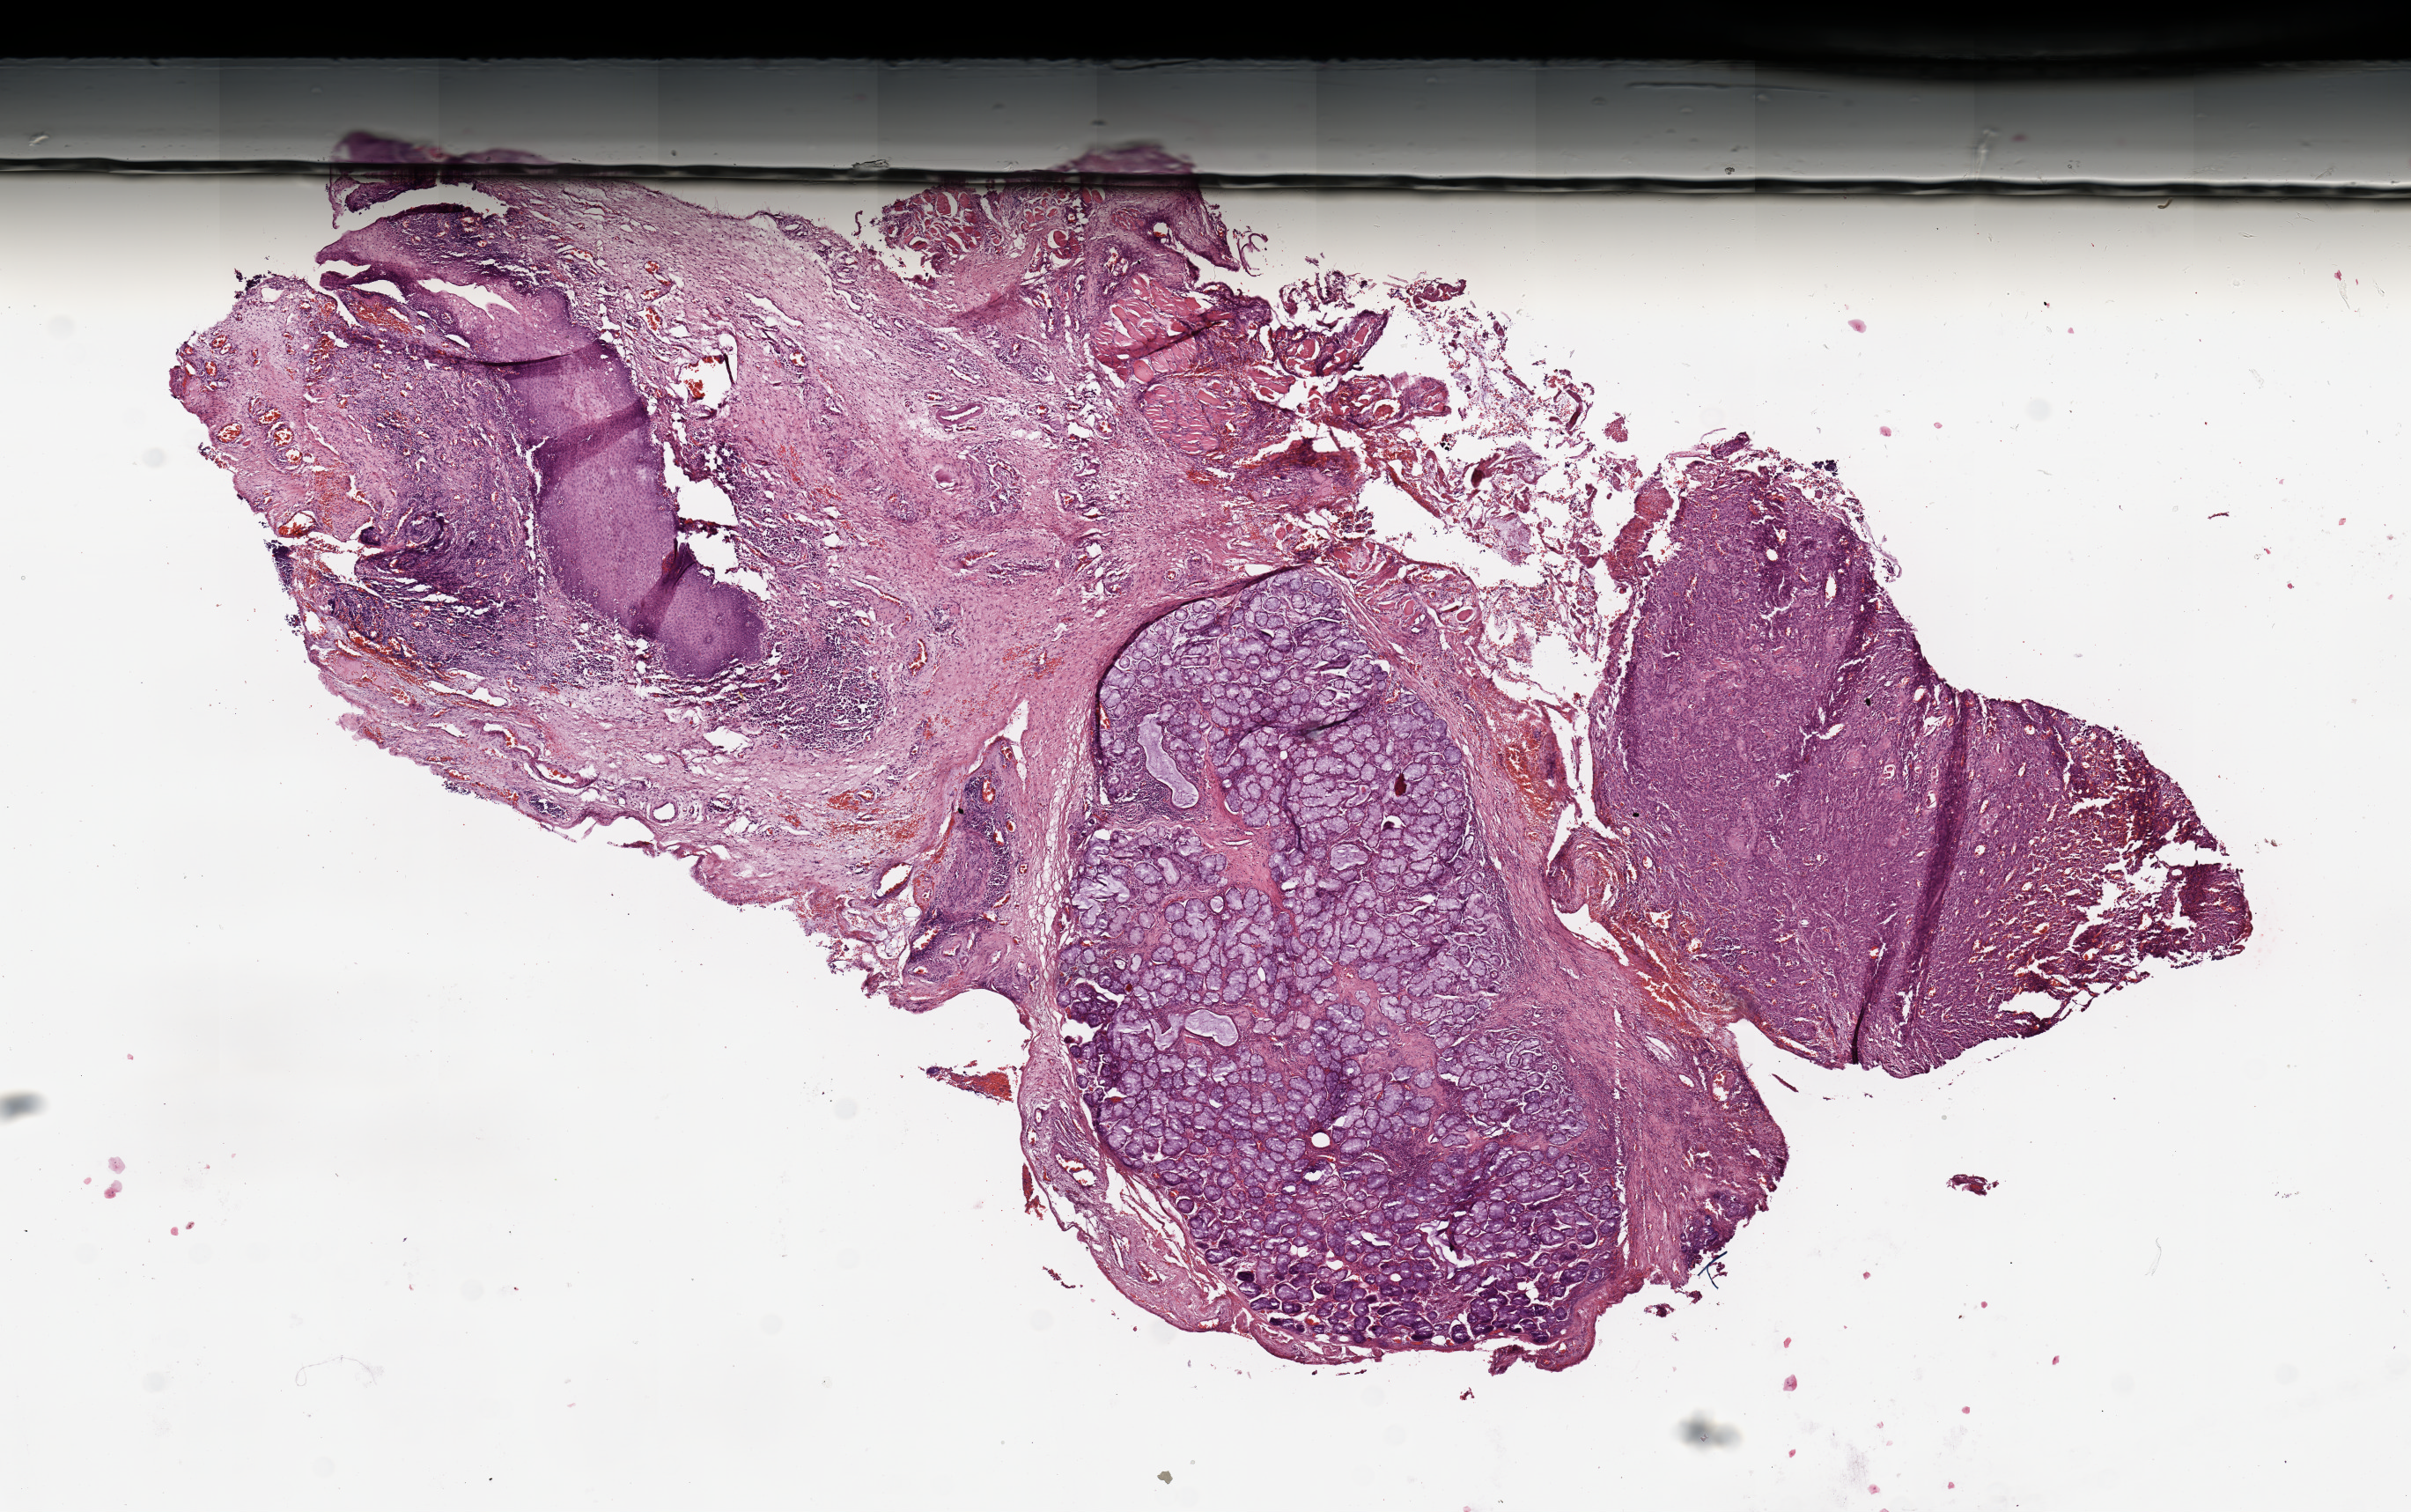
Hematoxylin and eosin (H&E) stained whole-slide image, a low-resolution overview of the entire scanned area, about 10.8 x 6.8 mm; head and neck, tissue type not recorded. Patient: male, age 51 years.
Patient diagnosis: Squamous cell carcinoma, NOS.